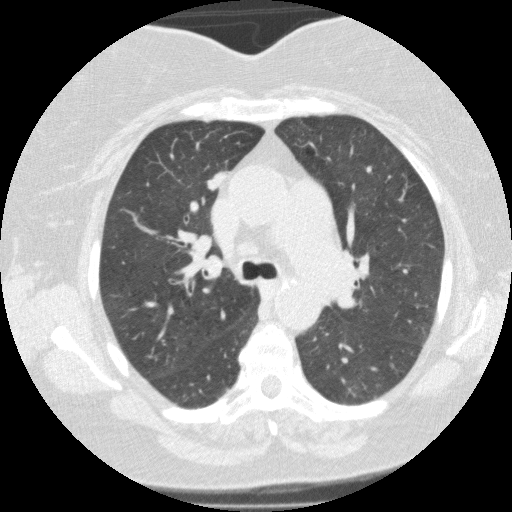
Low-dose screening chest CT, one axial slice; slice 95 of 146 in the series (ordered by position); lung window (W 1500 / L -600 HU); 2 mm slice thickness; 512 × 512 image matrix, field of view 330 × 330 mm.
Annotated regions visible in this slice (manually delineated by an expert):
- lesion 2 (tumor, upper lobe of right lung): bounding box [x1, y1, x2, y2] px = [206, 170, 228, 190]